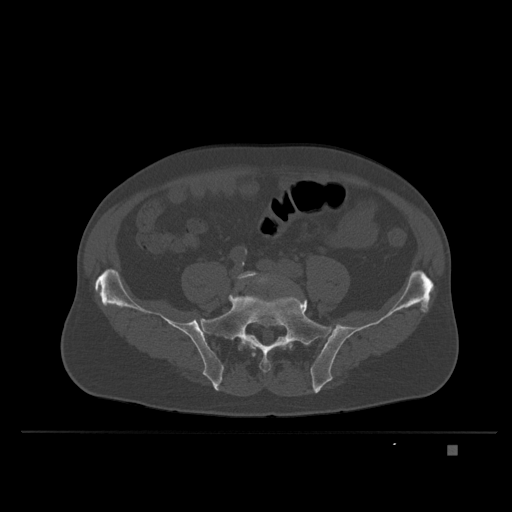
CT including the spine, one axial slice; position 43 of 435 along the scan axis; bone window (W 1800 / L 400 HU); 1.5 mm slice thickness; 512 × 512 image matrix, field of view 434 × 434 mm. Male patient, age 73 years. From the clinical record (not read from this slice): primary cancer: skin.
Annotated regions visible in this slice (semi-automatic segmentation, software-assisted and operator-edited):
- L5 vertebra: bounding box <237,271,292,357> (left, top, right, bottom; pixels)